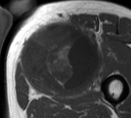
MRI of an extremity soft-tissue mass, one axial slice. MR volume resampled by the dataset authors to the PET/CT grid (not the native acquisition matrix). 3.27 mm slice thickness. 131 × 118 image matrix, field of view 128 × 115 mm. Male patient. From the clinical record (not read from this slice): histological type: pleiomorphic liposarcoma; grade: high; site of the primary tumour: left thigh.
Outlined on this slice (expert contour drawn on MRI and transferred to this co-registered scan by the dataset authors):
- gross tumour volume including surrounding oedema: bounding box <21,20,101,88> (left, top, right, bottom; pixels)
- gross tumour volume (mass): <21,25,97,88>